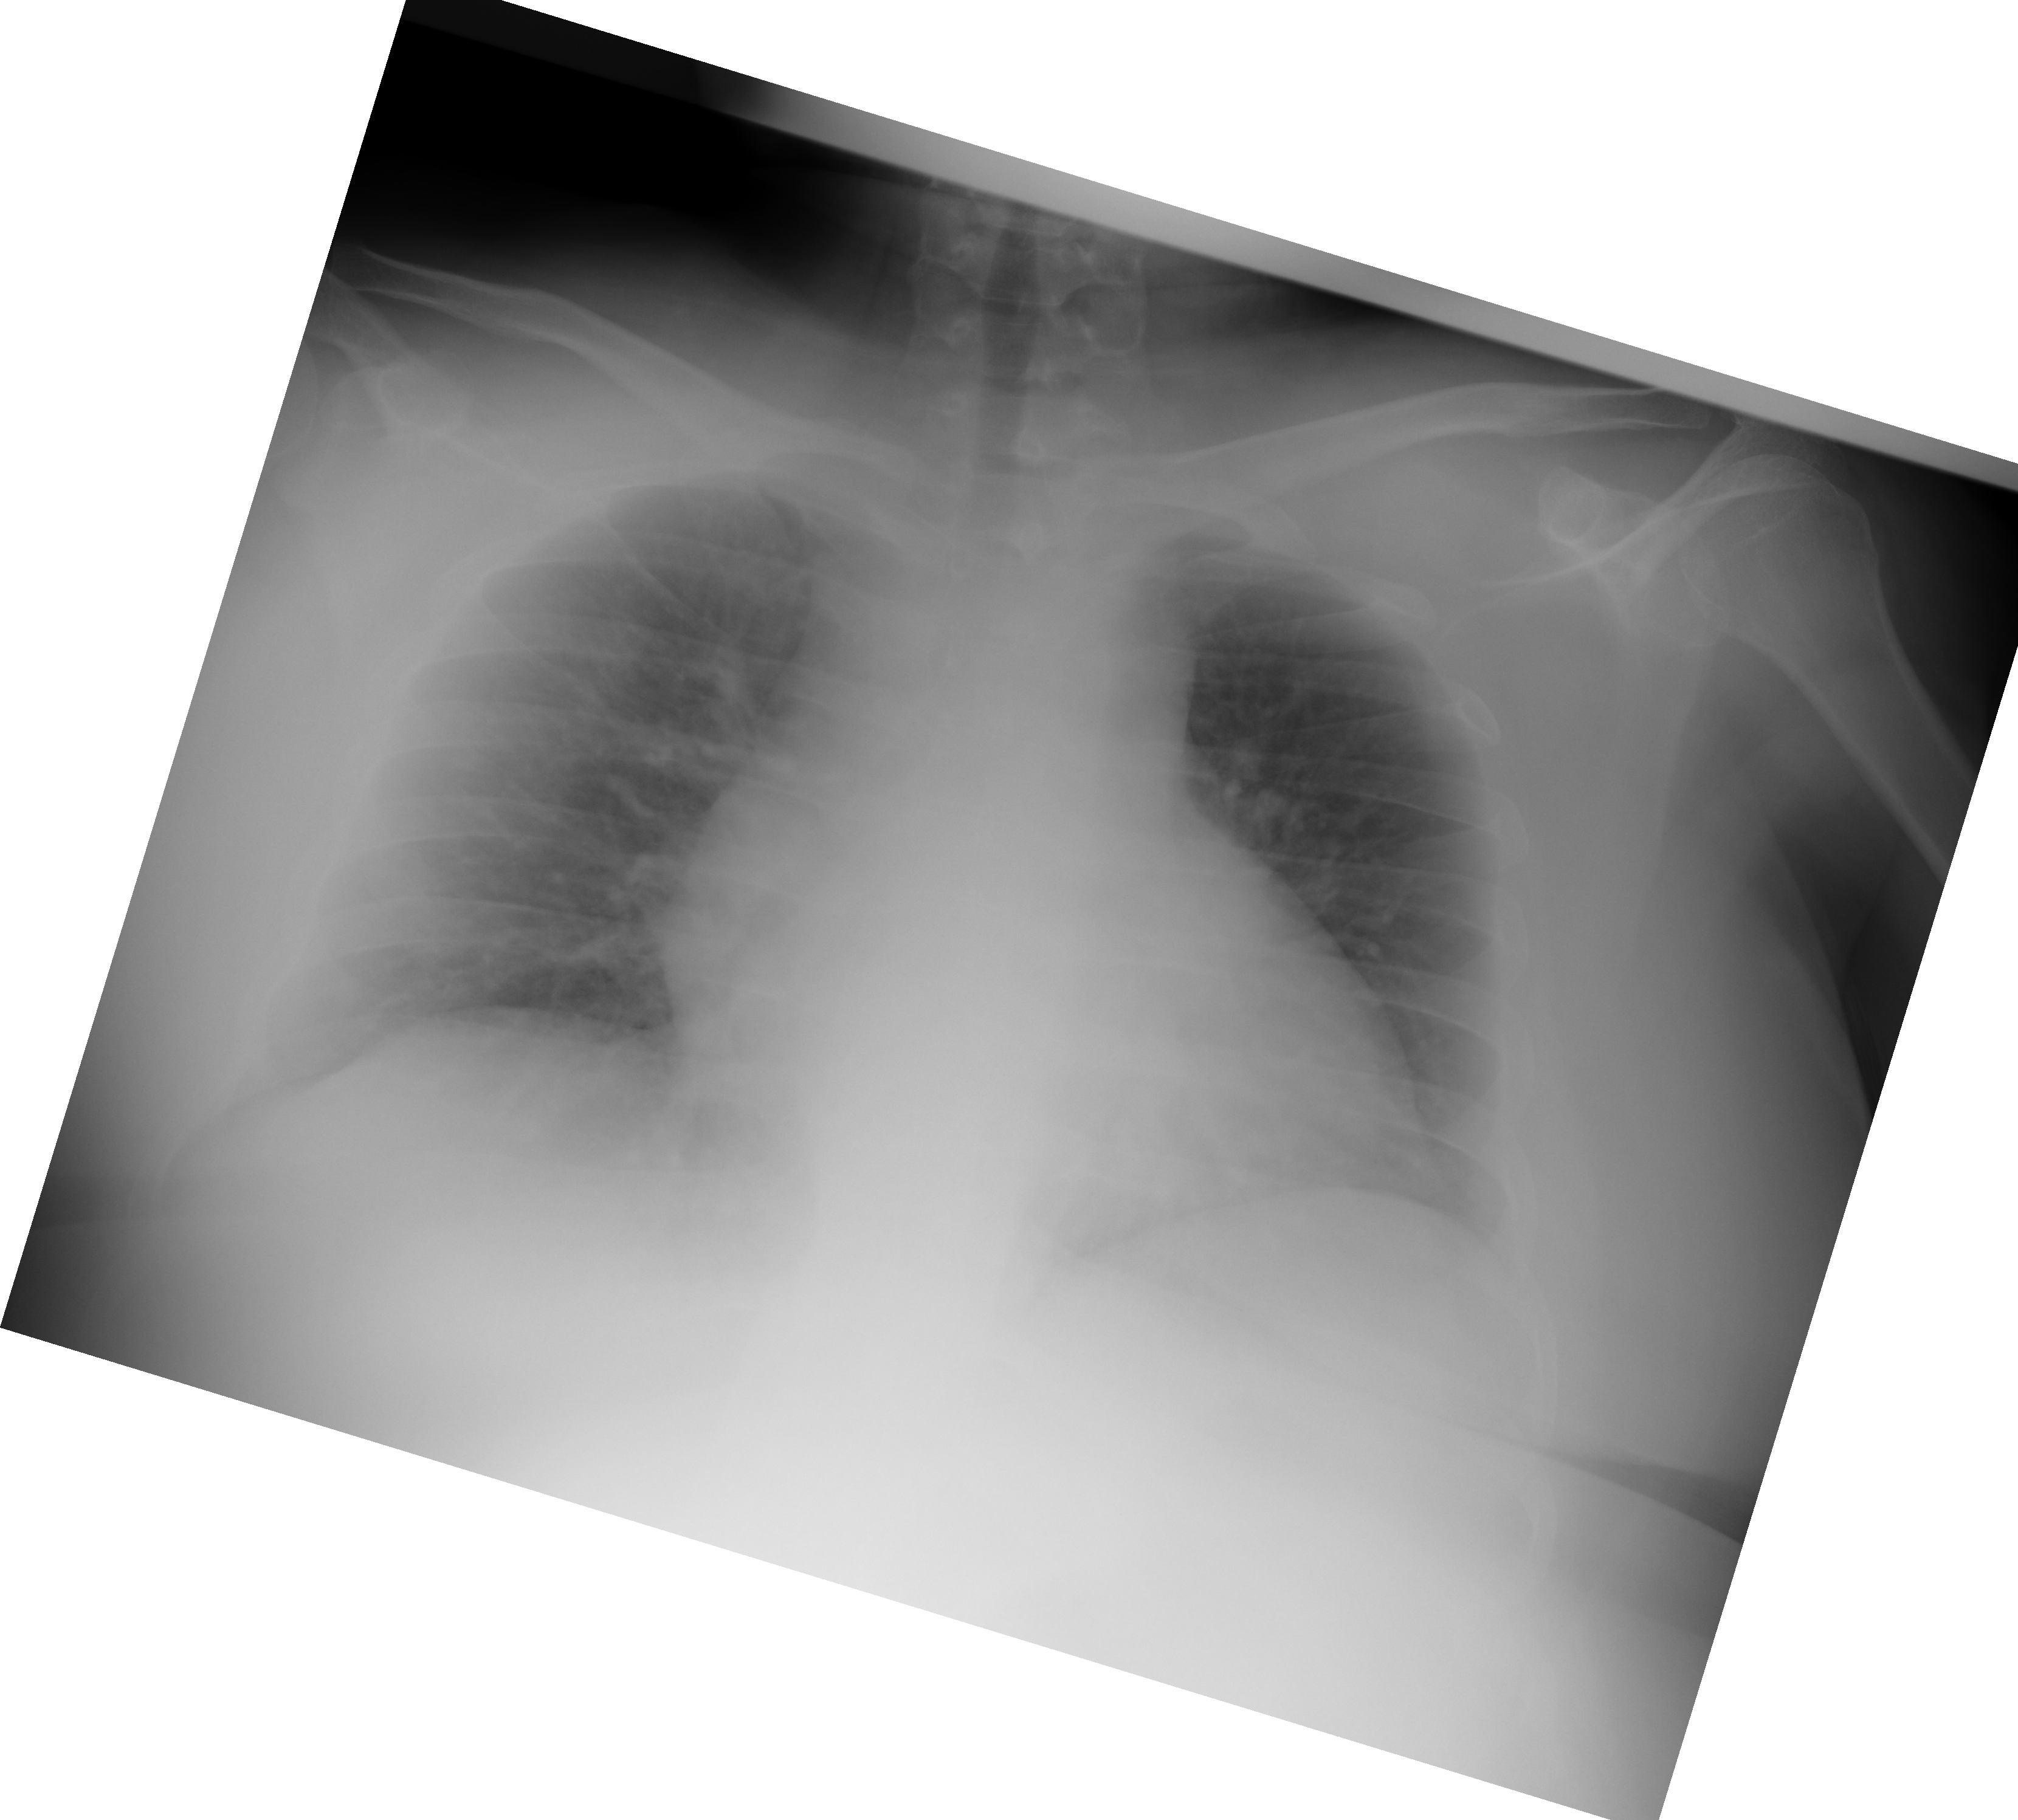
Portable chest radiograph, AP projection. Female patient, age 29 years; imaged 32 days after the COVID-19 diagnosis.
Radiologist's key findings for this exam: The lungs appear clear.